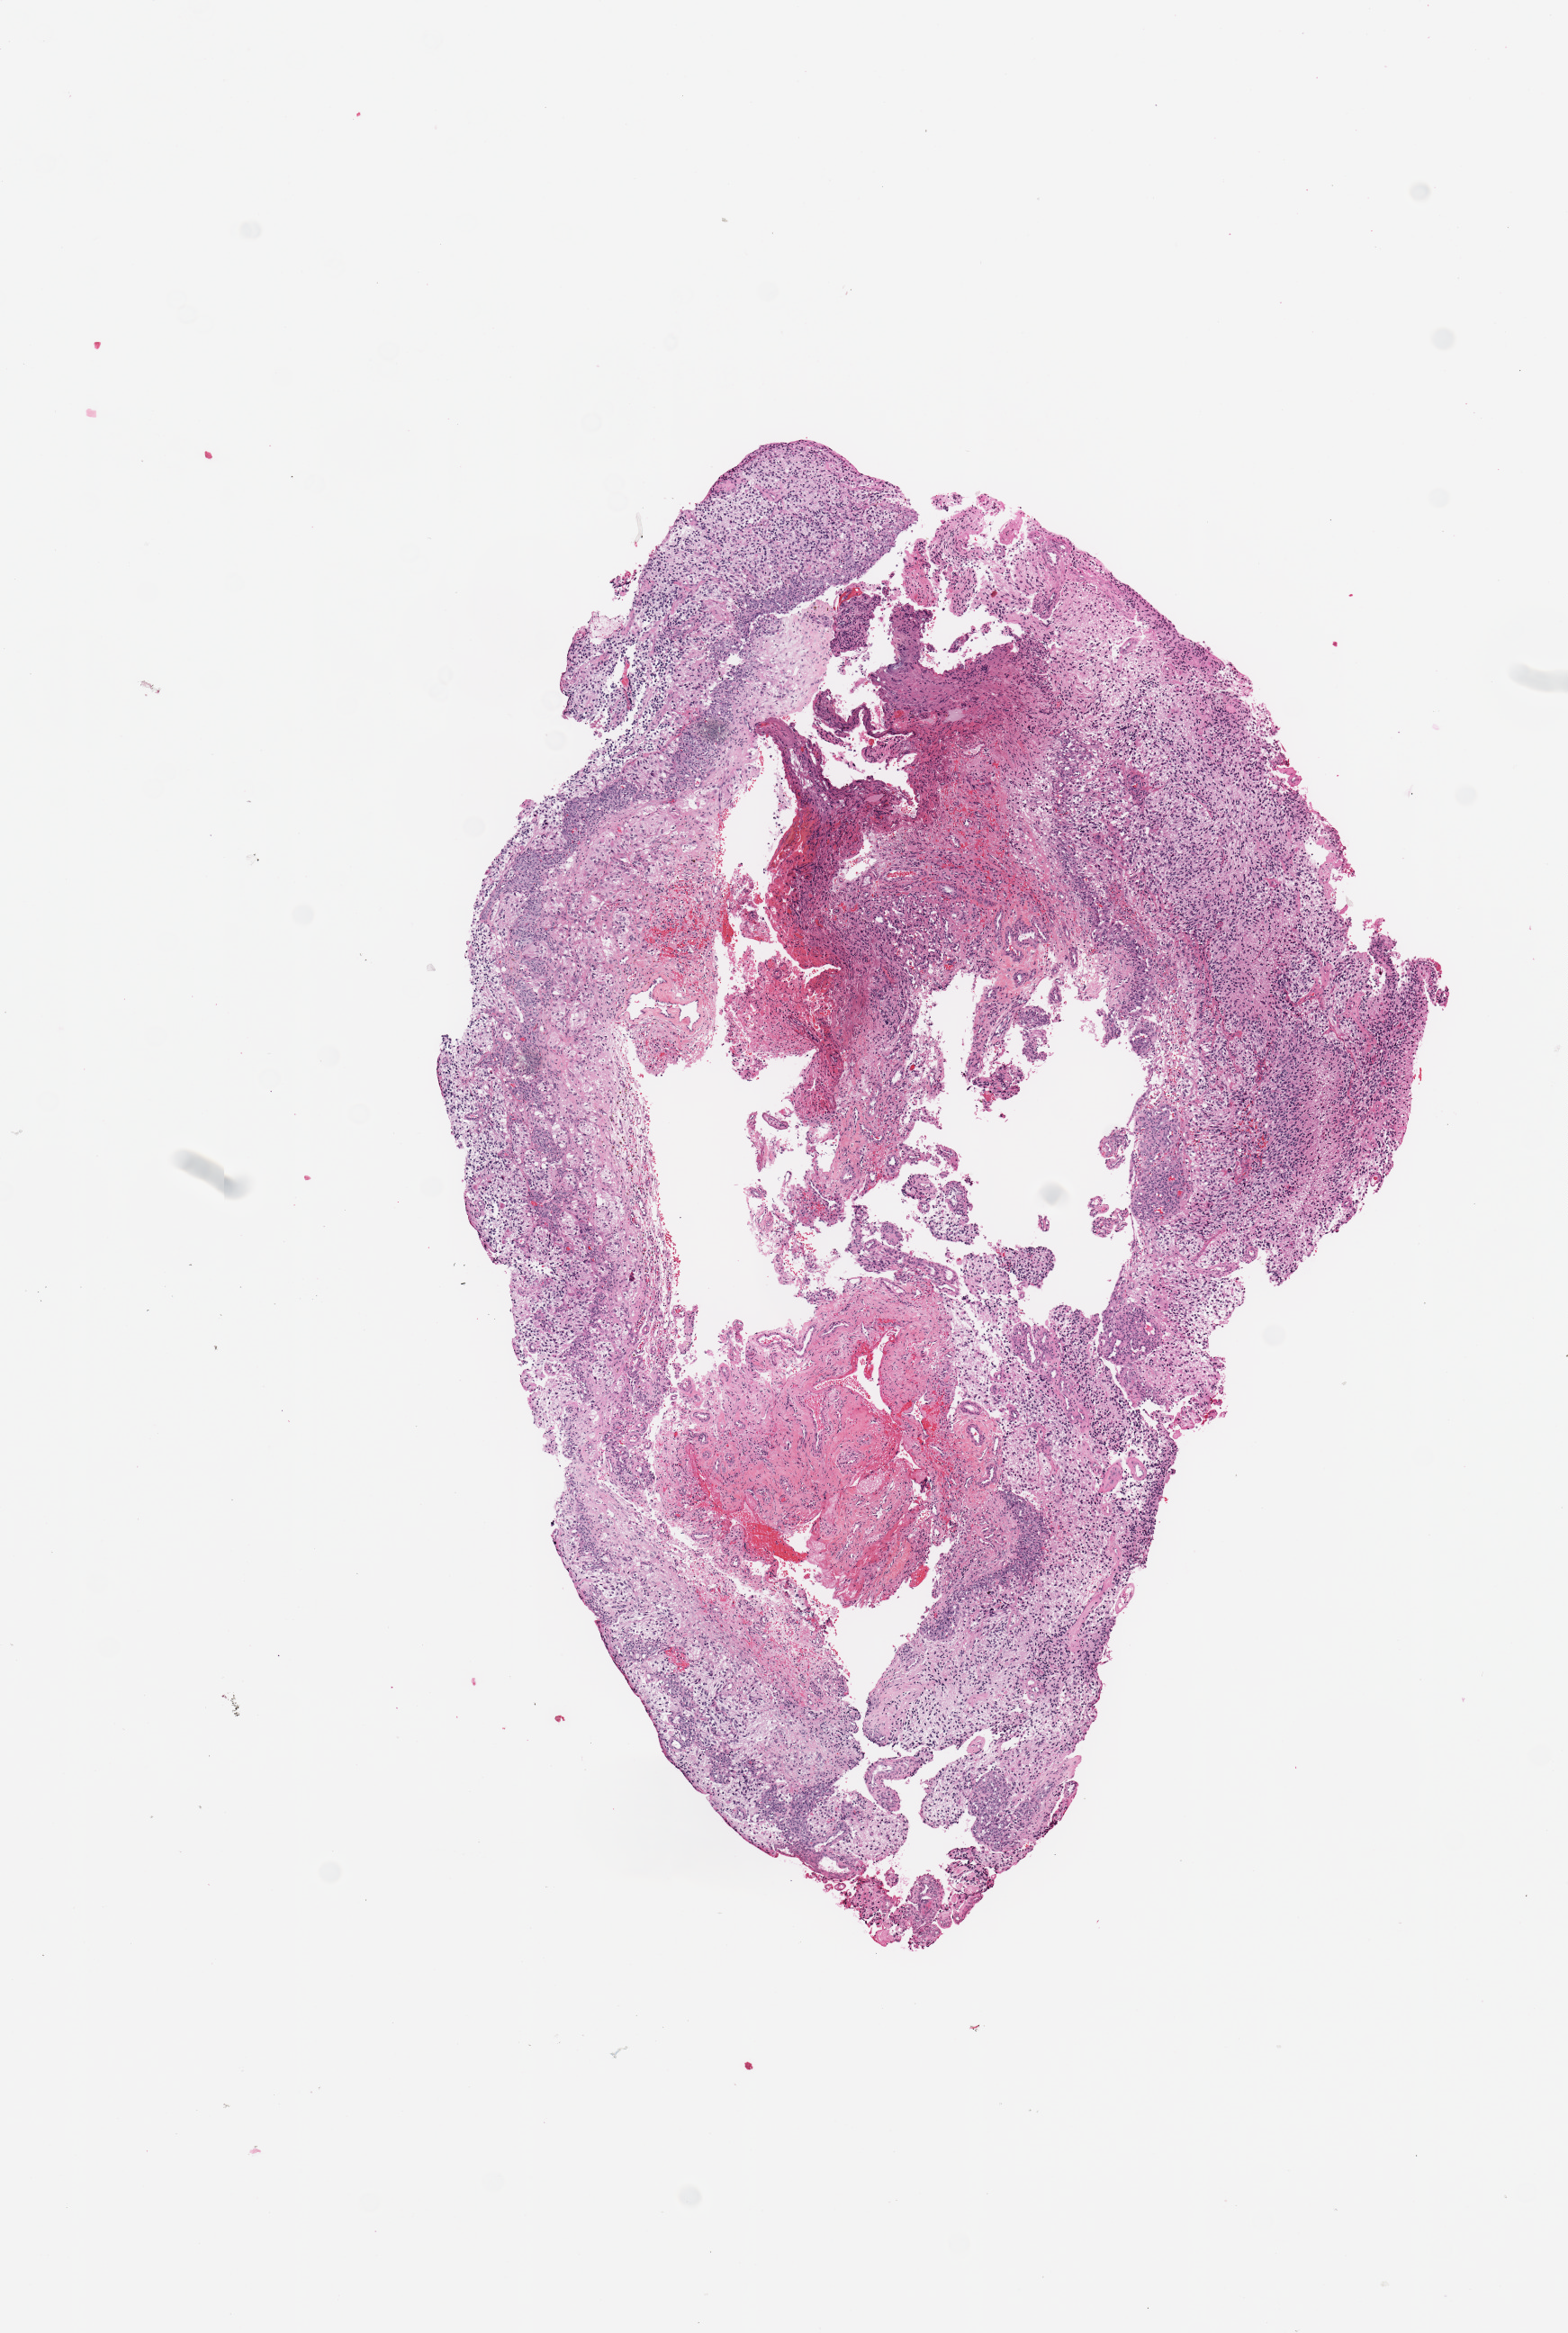
Digitized H&E tissue section (whole slide), shown as a low-resolution overview of the whole scanned area (about 6.9 x 10.3 mm, from a 20x scan). Tumour tissue sample, sampled site: frontal lobe. Patient: male, age 77 years. Composition of this section per pathologist review: tumour nuclei 65%, necrosis 5%.
Diagnosis: Glioblastoma. Primary tumour site (as recorded): frontal lobe.